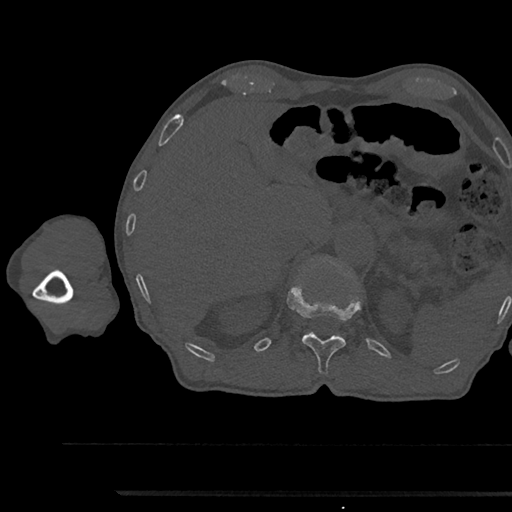
CT including the spine, one axial slice. Slice 698 of 797 in the series (ordered by position). Reconstruction kernel Br40s/3. 120 kVp. Bone window (W 1800 / L 400 HU). 0.5 mm slice thickness. 512 × 512 image matrix, field of view 367 × 367 mm. Male patient, age 79 years. Case-level facts recorded for this patient, not image findings: primary cancer: prostate.
Annotated regions visible in this slice (semi-automatic segmentation, software-assisted and operator-edited):
- T12 vertebra: bounding box (x1, y1, x2, y2) in pixels: (287, 288, 360, 374)